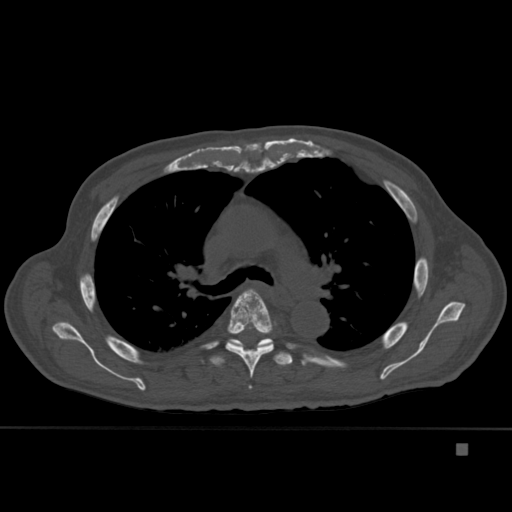
CT including the spine, one axial slice. Slice 305 of 451 in the series (ordered by position). Bone window (W 1800 / L 400 HU). 512 × 512 image matrix, field of view 378 × 378 mm. Male patient, age 75 years. Case-level facts recorded for this patient, not image findings: primary cancer: prostate.
Outlined on this slice (semi-automatic segmentation, software-assisted and operator-edited):
- T4 vertebra: bounding box (x1, y1, x2, y2) in pixels: (249, 385, 252, 389)
- T5 vertebra: (225, 289, 276, 378)
- T6 vertebra: (210, 338, 293, 367)